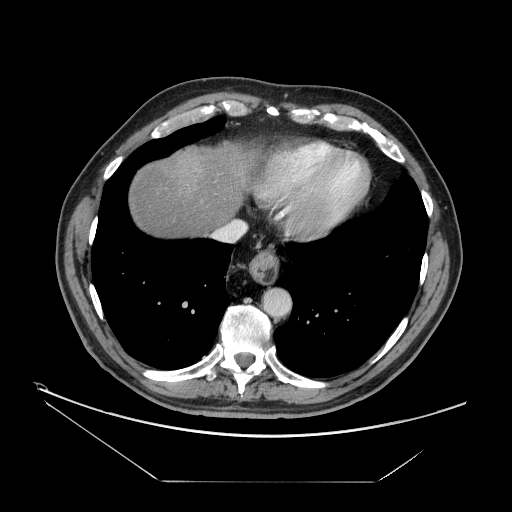
Contrast-enhanced abdominal CT, one axial slice; position 147 of 161 along the scan axis; 120 kVp; intravenous contrast given; soft-tissue window (W 400 / L 40 HU); 2.5 mm slice thickness; 512 × 512 image matrix, field of view 440 × 440 mm. Male patient, age 65 years. From the clinical record (not read from this slice): diagnosis: colorectal cancer liver metastases, imaged before liver resection; multiple liver metastases: yes.
Structures marked on this image (expert manual segmentation):
- hepatic veins: bounding box [x1, y1, x2, y2] px = [215, 221, 247, 241]
- liver: [128, 144, 249, 238]
- planned liver remnant (the part of the liver to remain after resection): [128, 144, 249, 238]